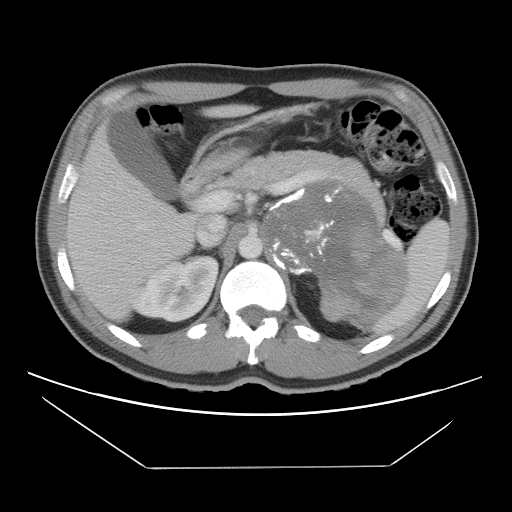
Contrast-enhanced abdominal CT, one axial slice; slice 71 of 131 in the series (ordered by position); intravenous contrast given; soft-tissue window (W 400 / L 40 HU); 5 mm slice thickness; 512 × 512 image matrix, field of view 396 × 396 mm. Male patient, age 44 years. From the clinical record (not read from this slice): diagnosis: adrenocortical carcinoma; tumour side: left adrenal; tumour size at pathology: 15.5 cm; Ki-67 index: 6 %; stage (as recorded): 2.
Annotated regions visible in this slice (semi-automatic segmentation, software-assisted and operator-edited):
- mass: box from (x=262, y=181) to (x=405, y=326) px